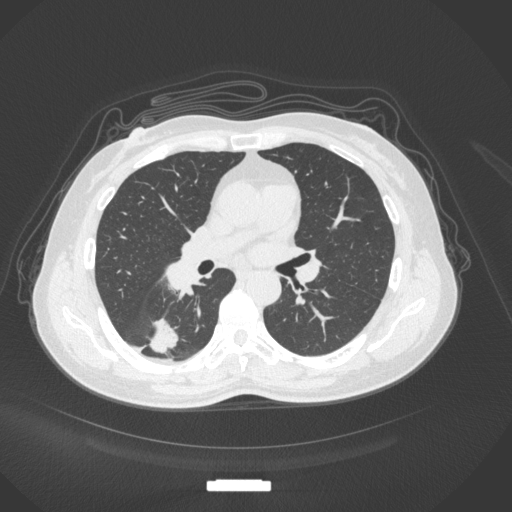
Chest CT, one axial slice. Slice 168 of 352 in the series (ordered by position). Reconstruction kernel B31f. 120 kVp. Lung window (W 1500 / L -600 HU). 1 mm slice thickness. 512 × 512 image matrix, field of view 400 × 400 mm. Patient: female, 55 years. Case-level facts recorded for this patient, not image findings: clinical TNM (as recorded): T1c N1 M0.
Structures marked on this image (bounding box drawn by a radiologist):
- lung tumour (recorded histology: adenocarcinoma): box from (x=149, y=315) to (x=181, y=355) px